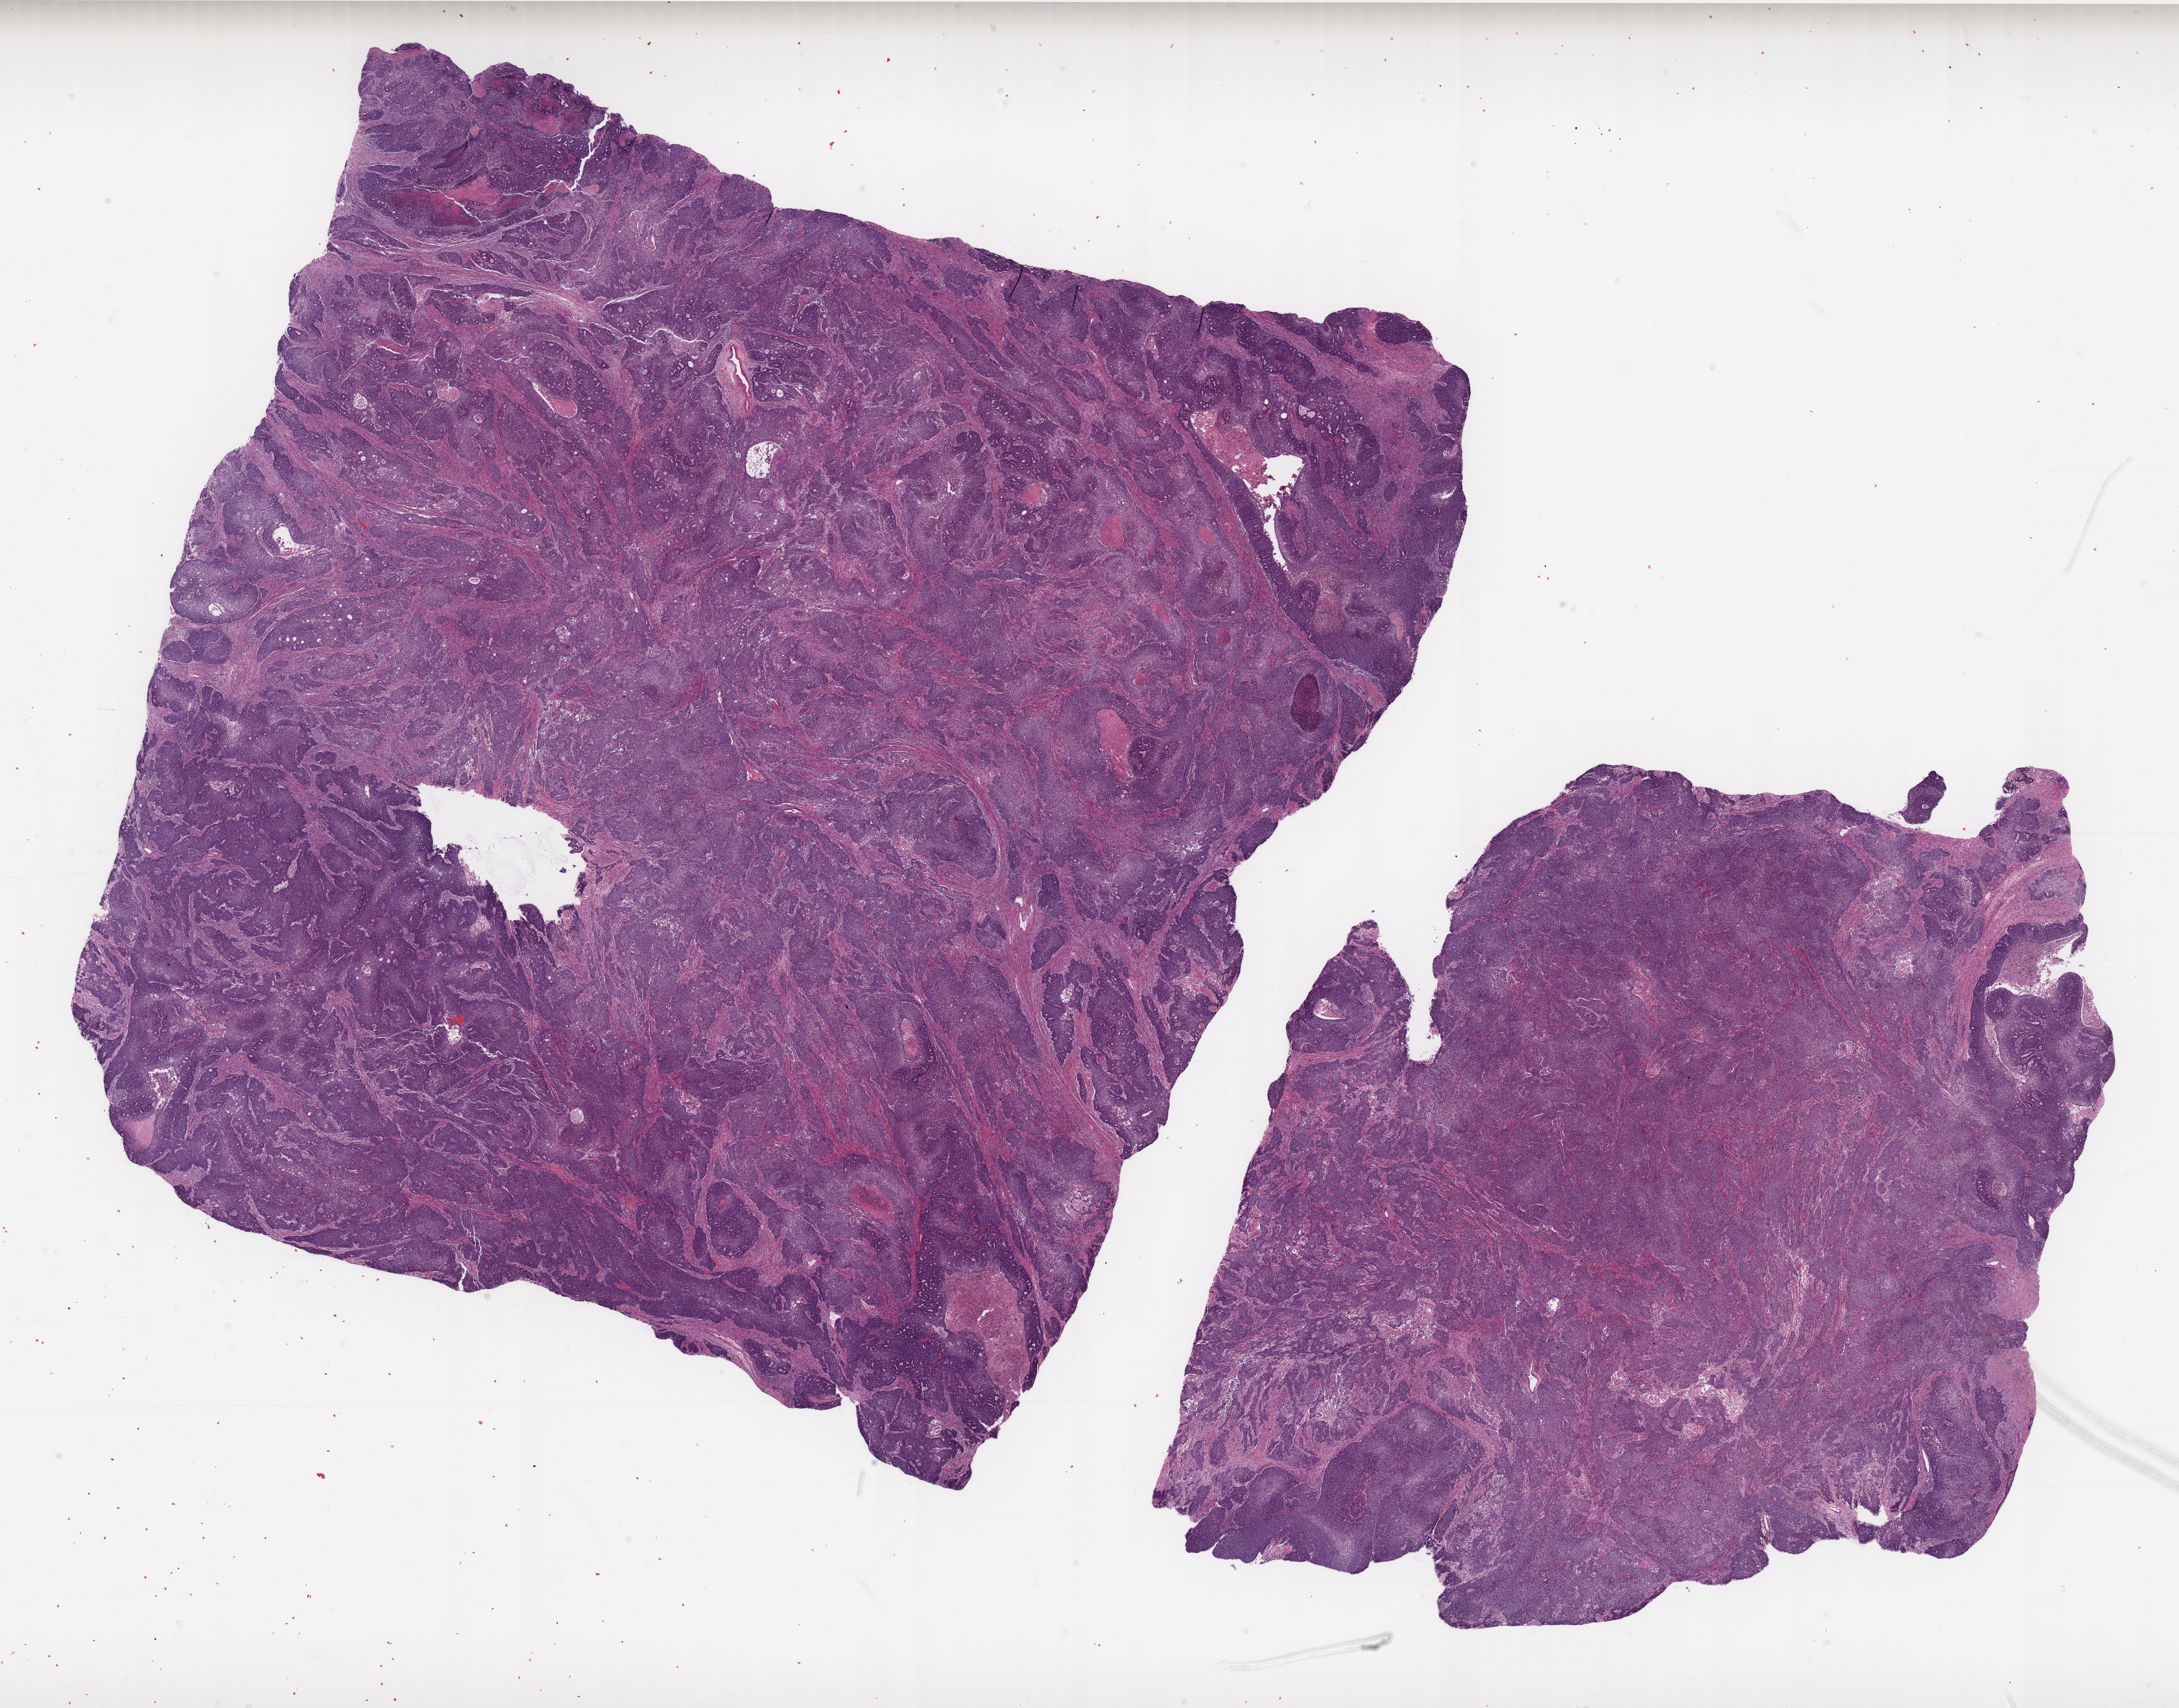
Digitized H&E tissue section (whole slide) — whole scanned area (about 26.9 x 21.1 mm, acquisition: 40x scan) shown as a low-resolution overview, formalin-fixed paraffin-embedded (FFPE) diagnostic section, uterus, primary tumour sample. Female patient; age at initial diagnosis 68 years. Histologic grade: G3 (poorly differentiated).
• histologic diagnosis: Endometrioid adenocarcinoma, NOS (endometrium)
• FIGO stage: IIIA